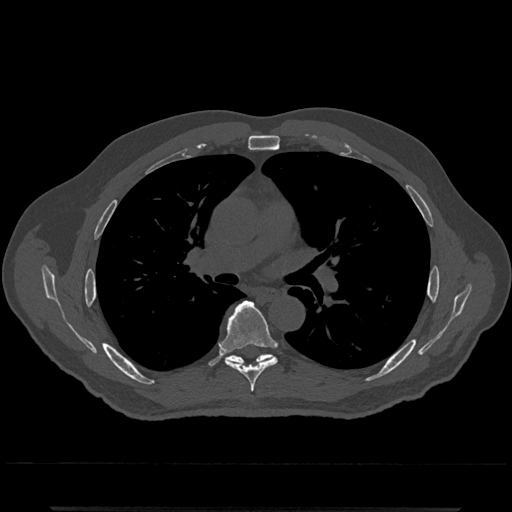
CT including the spine, one axial slice. Slice 760 of 797 in the series (ordered by position). 120 kVp. Bone window (W 1800 / L 400 HU). 0.5 mm slice thickness. 512 × 512 image matrix, field of view 393 × 393 mm. Male patient, age 67 years. Case-level facts recorded for this patient, not image findings: primary cancer: prostate.
Structures marked on this image (semi-automatically segmented with operator editing):
- T6 vertebra: bounding box (x1, y1, x2, y2) in pixels: (221, 301, 277, 399)
- T7 vertebra: (227, 354, 272, 365)